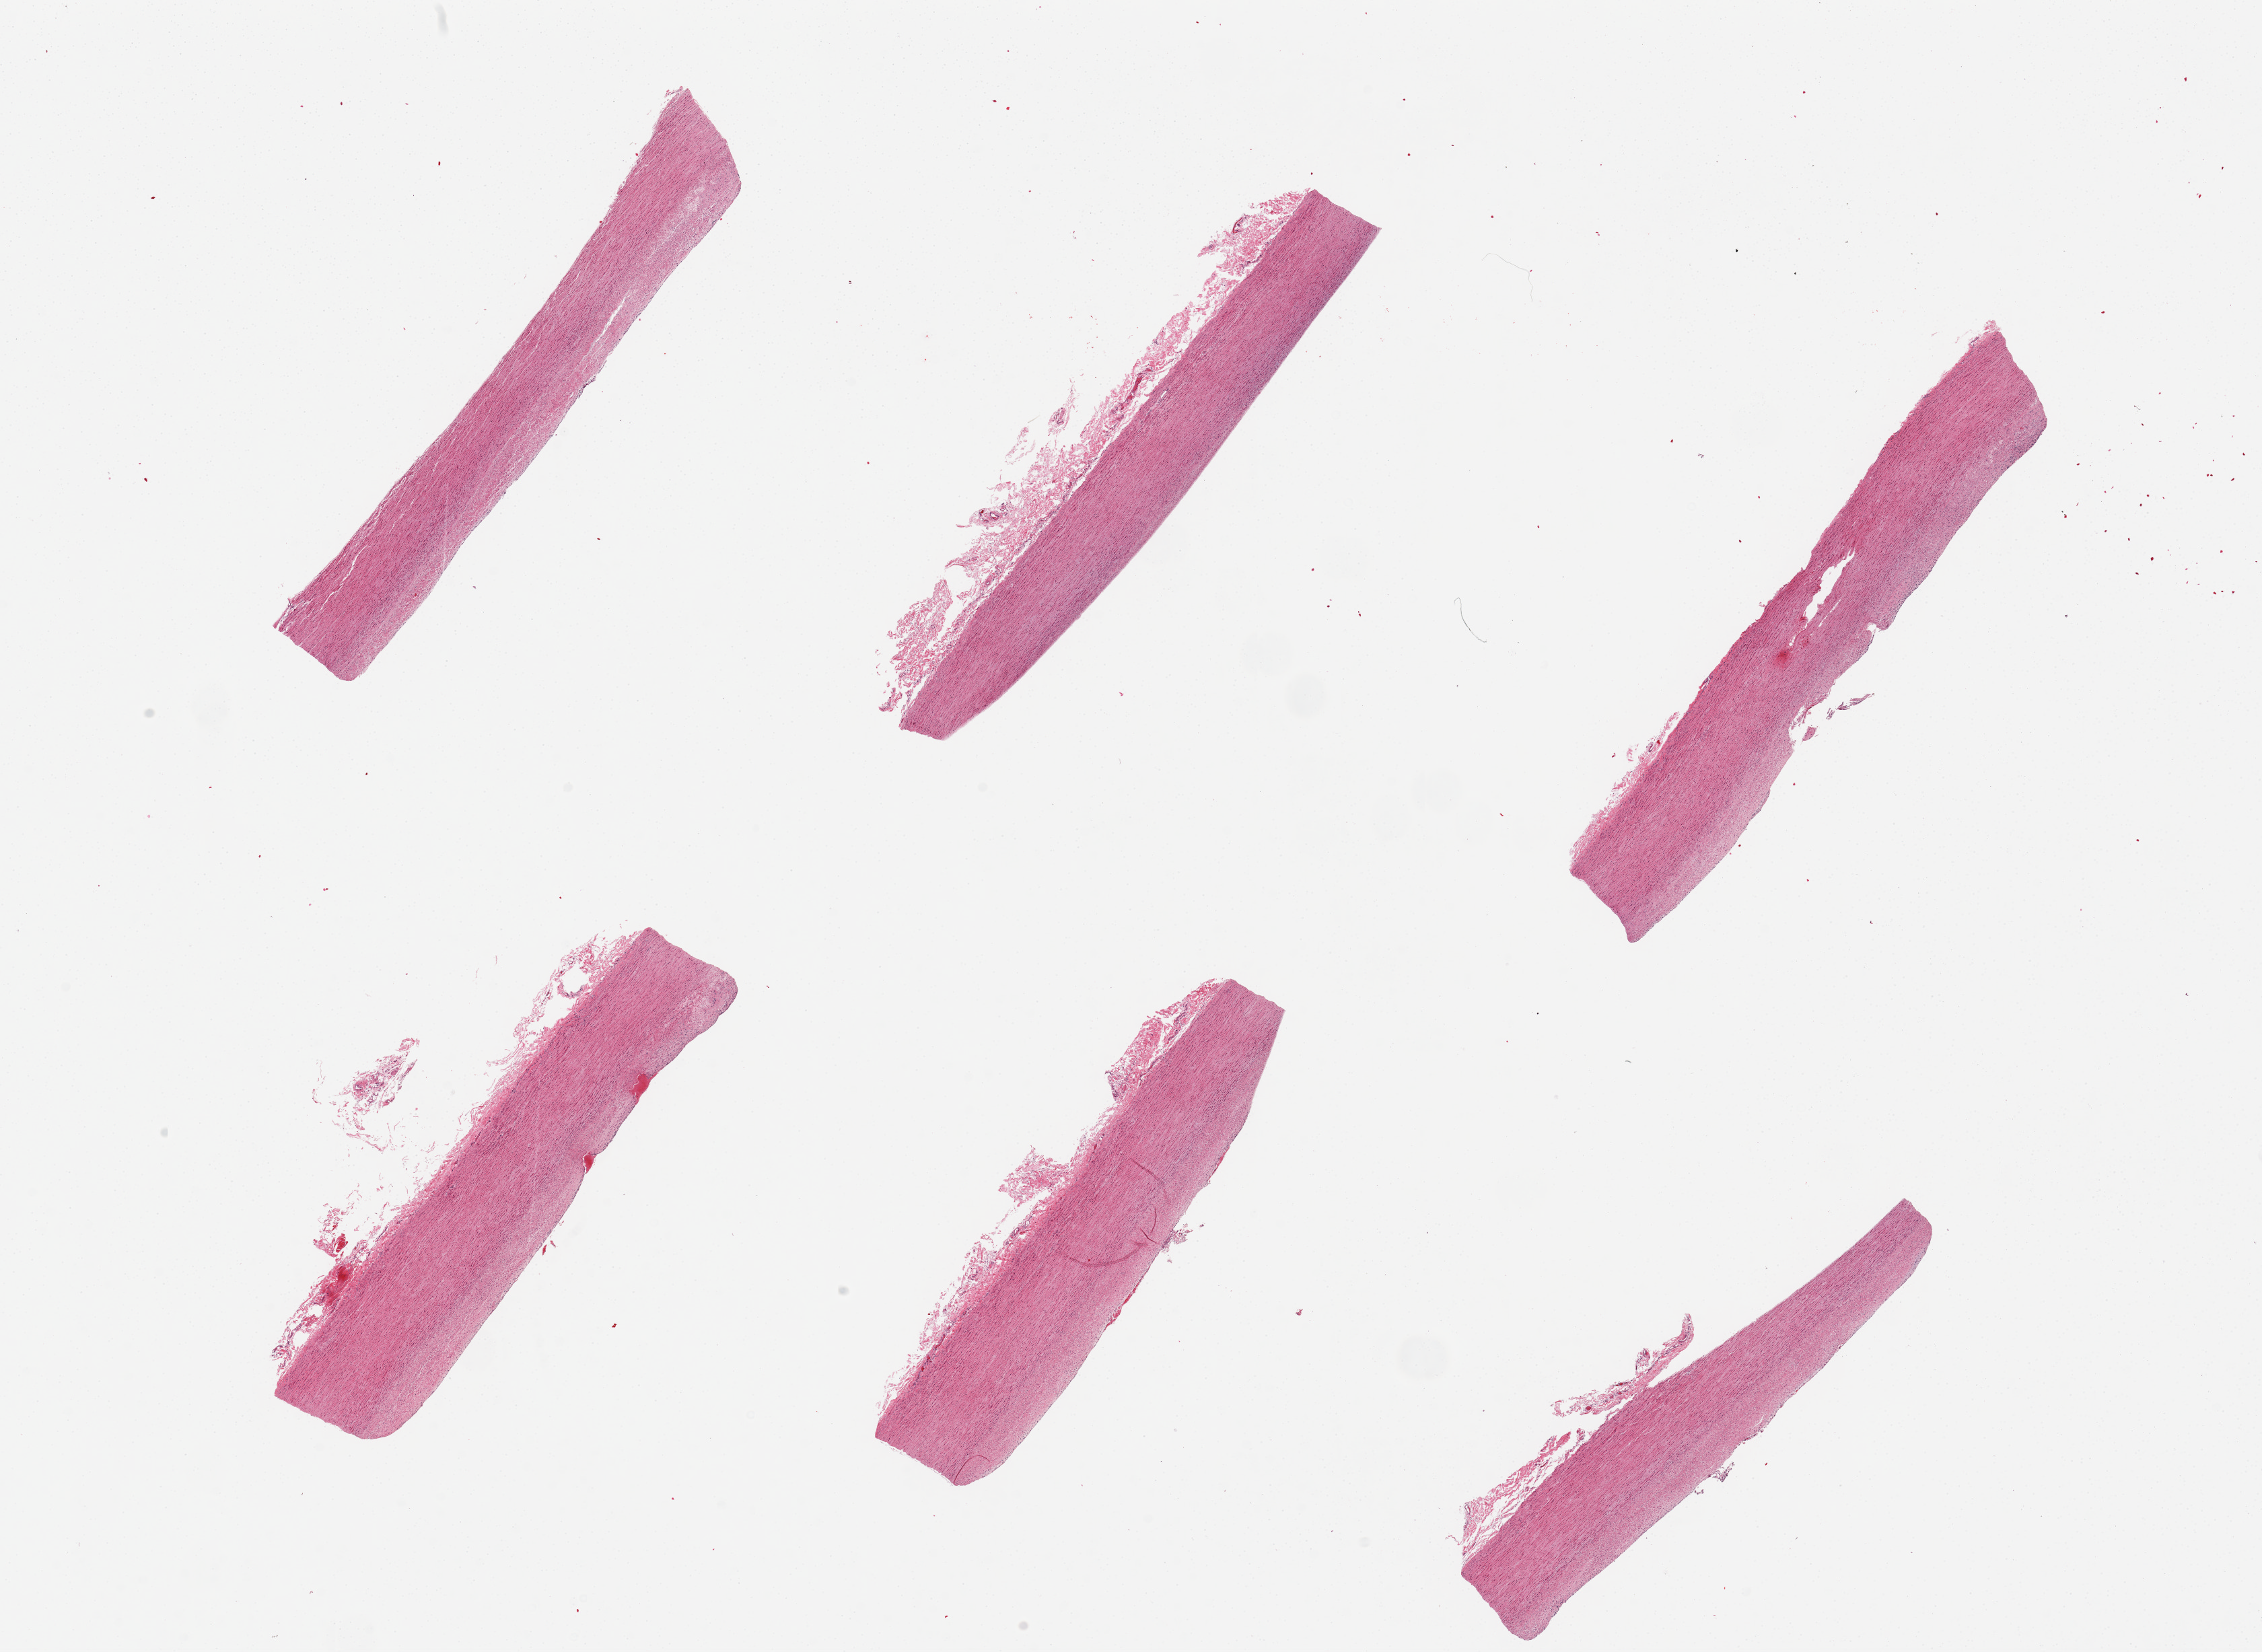
Whole-slide image, haematoxylin and eosin stain, brightfield — whole scanned area (about 26.6 x 19.4 mm) shown as a low-resolution overview. PAXgene-fixed paraffin-embedded (PFPE) section. Target tissue: aorta. Tissue donor sample.
Reviewer comment on this tissue sample: 6 pieces. Mostly well trimmed.